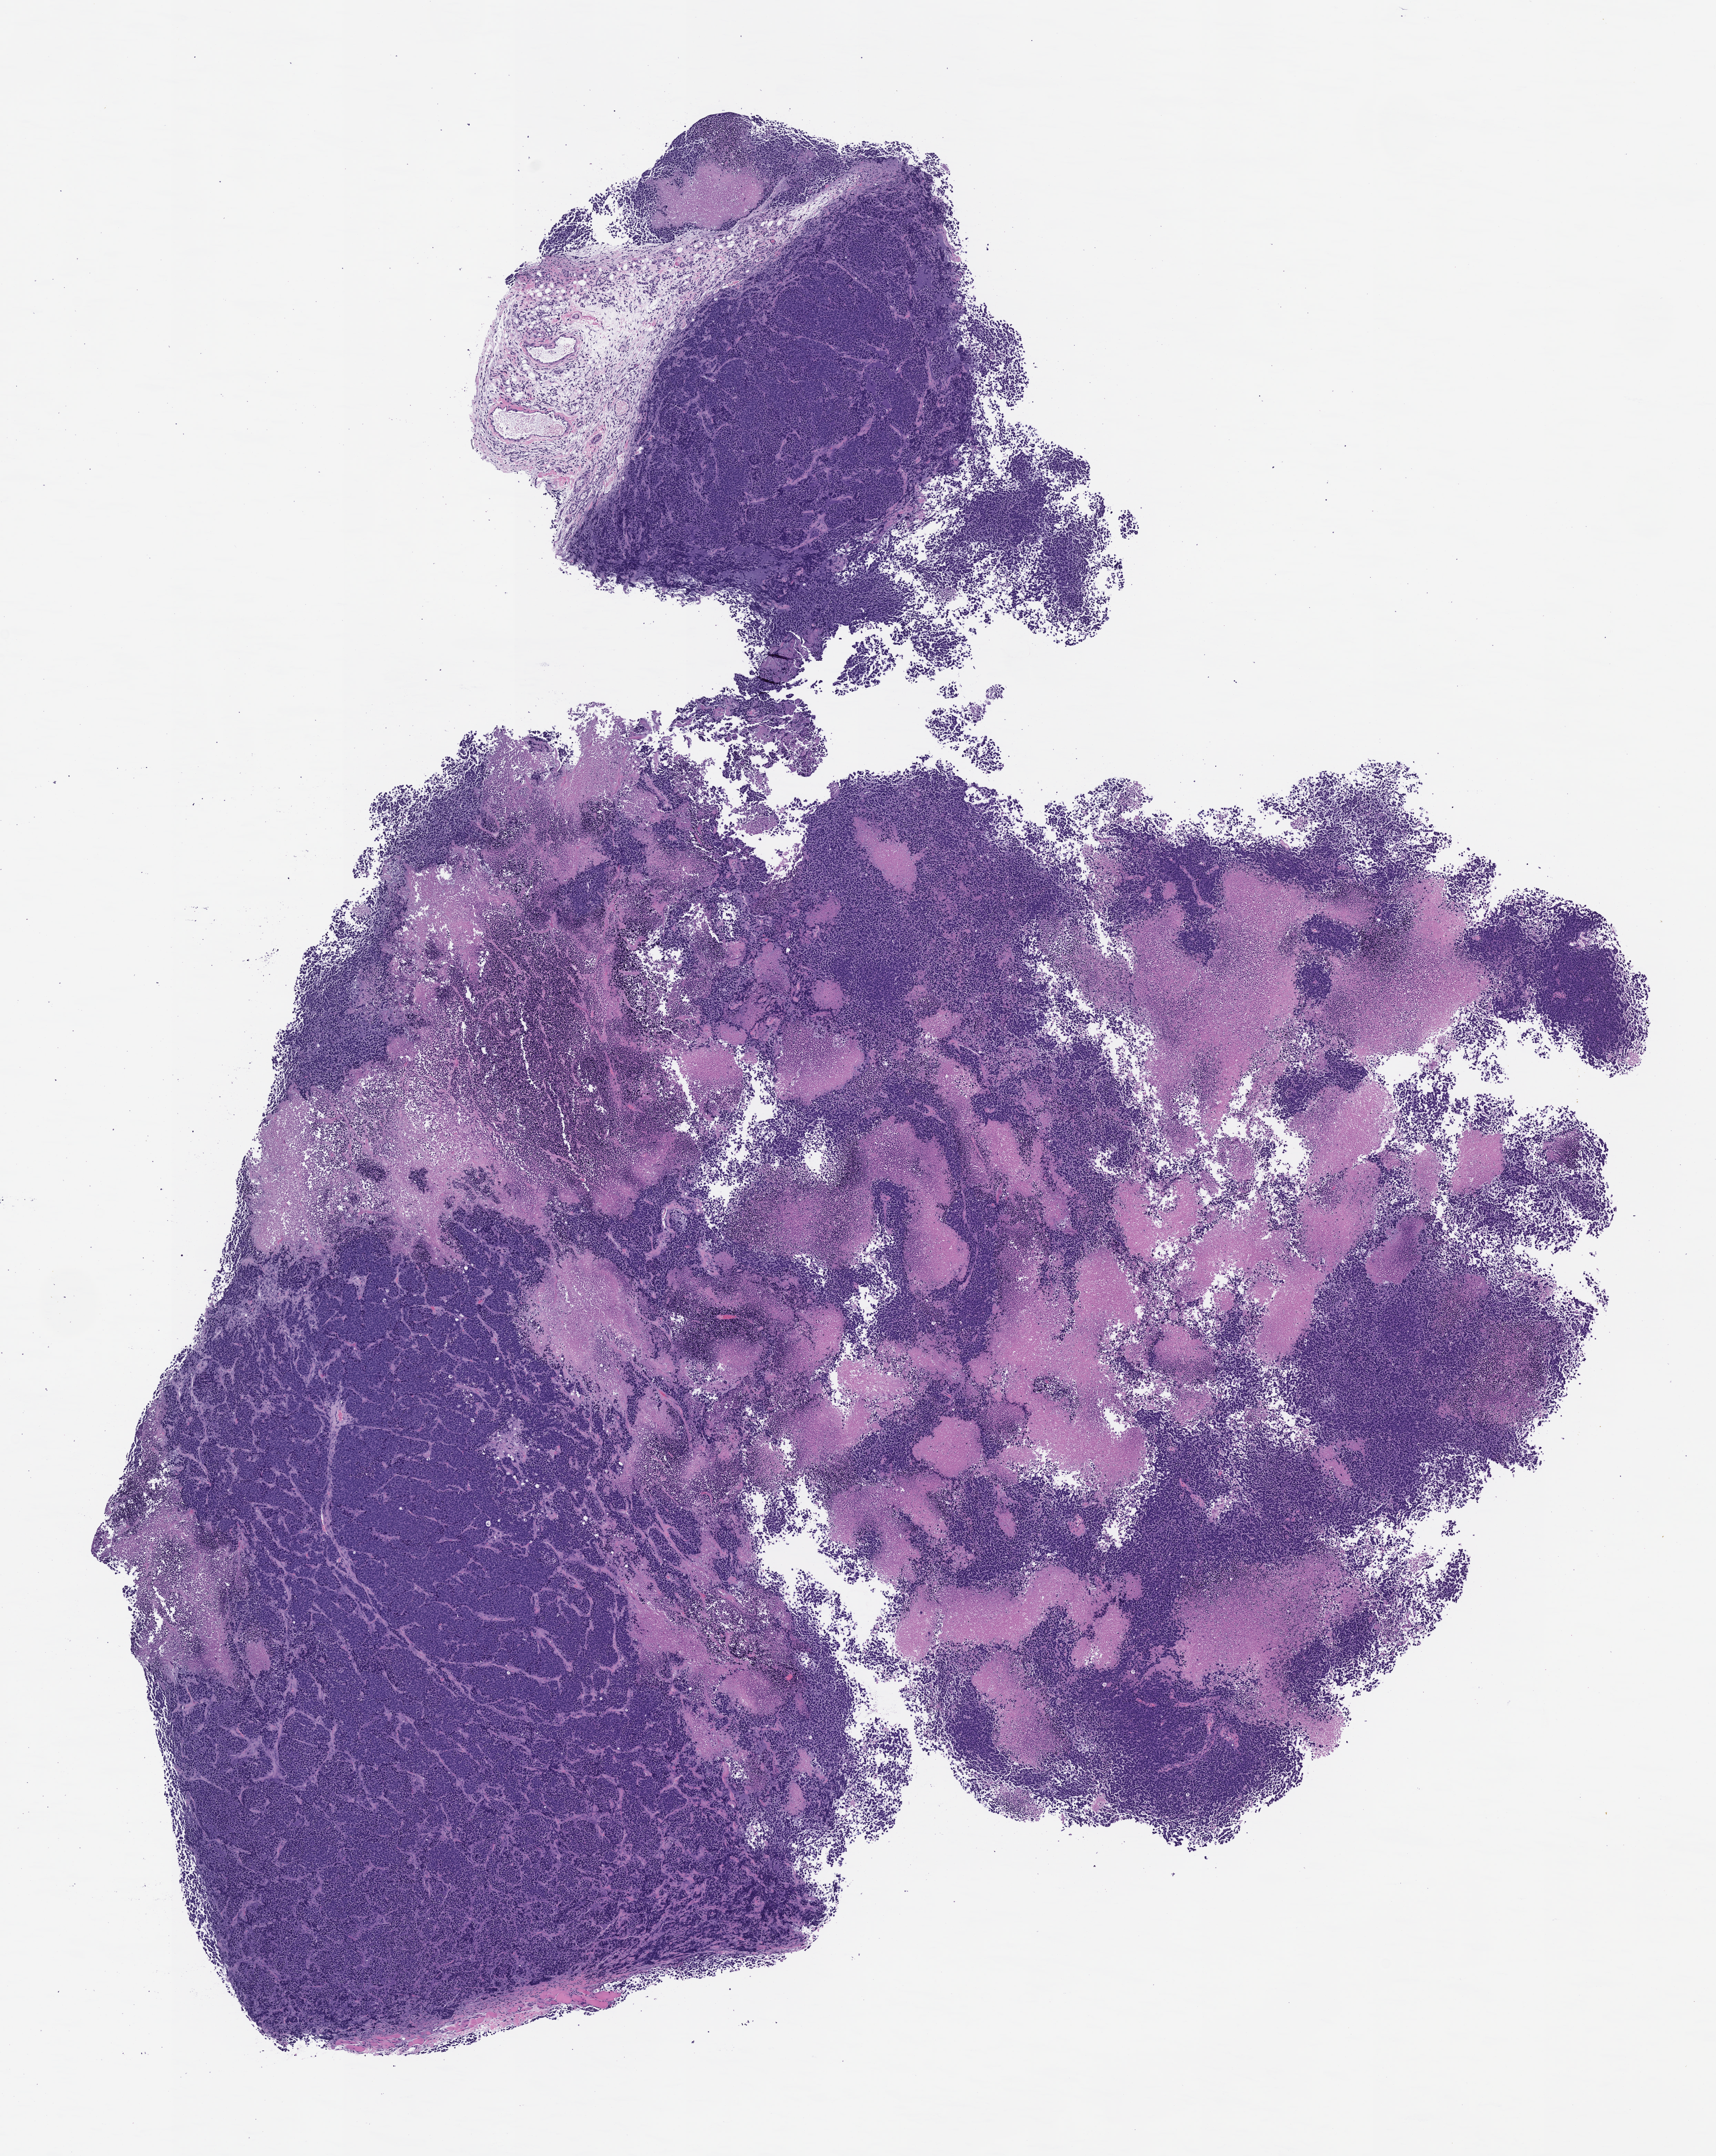
Hematoxylin and eosin (H&E) whole-slide image of a patient-derived xenograft (PDX) tumor grown in a mouse, passage 1, whole scanned area (about 10.0 x 12.6 mm) shown as a low-resolution overview, formalin-fixed, paraffin-embedded (FFPE) tissue, tumor site category: neuroendocrine system.
Originating patient diagnosis: Neuroendocrine Carcinoma.